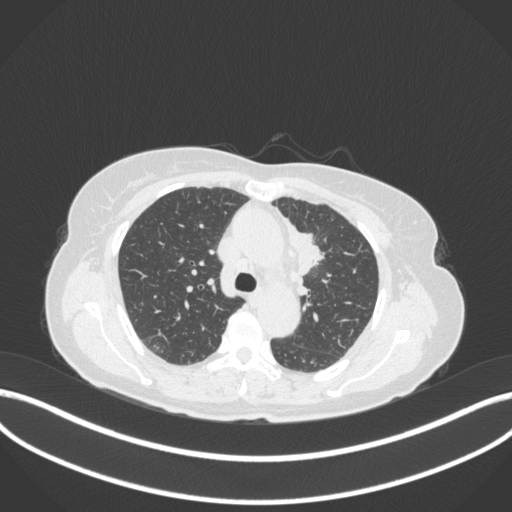
Chest CT, one axial slice. Slice 231 of 368 in the series (ordered by position). Lung window (W 1500 / L -600 HU). 1 mm slice thickness. 512 × 512 image matrix. Female patient, age 65 years. From the clinical record (not read from this slice): clinical TNM (as recorded): T2a N0 M0.
Outlined on this slice (bounding box drawn by a radiologist):
- lung tumour (recorded histology: adenocarcinoma): box from (x=282, y=215) to (x=327, y=279) px